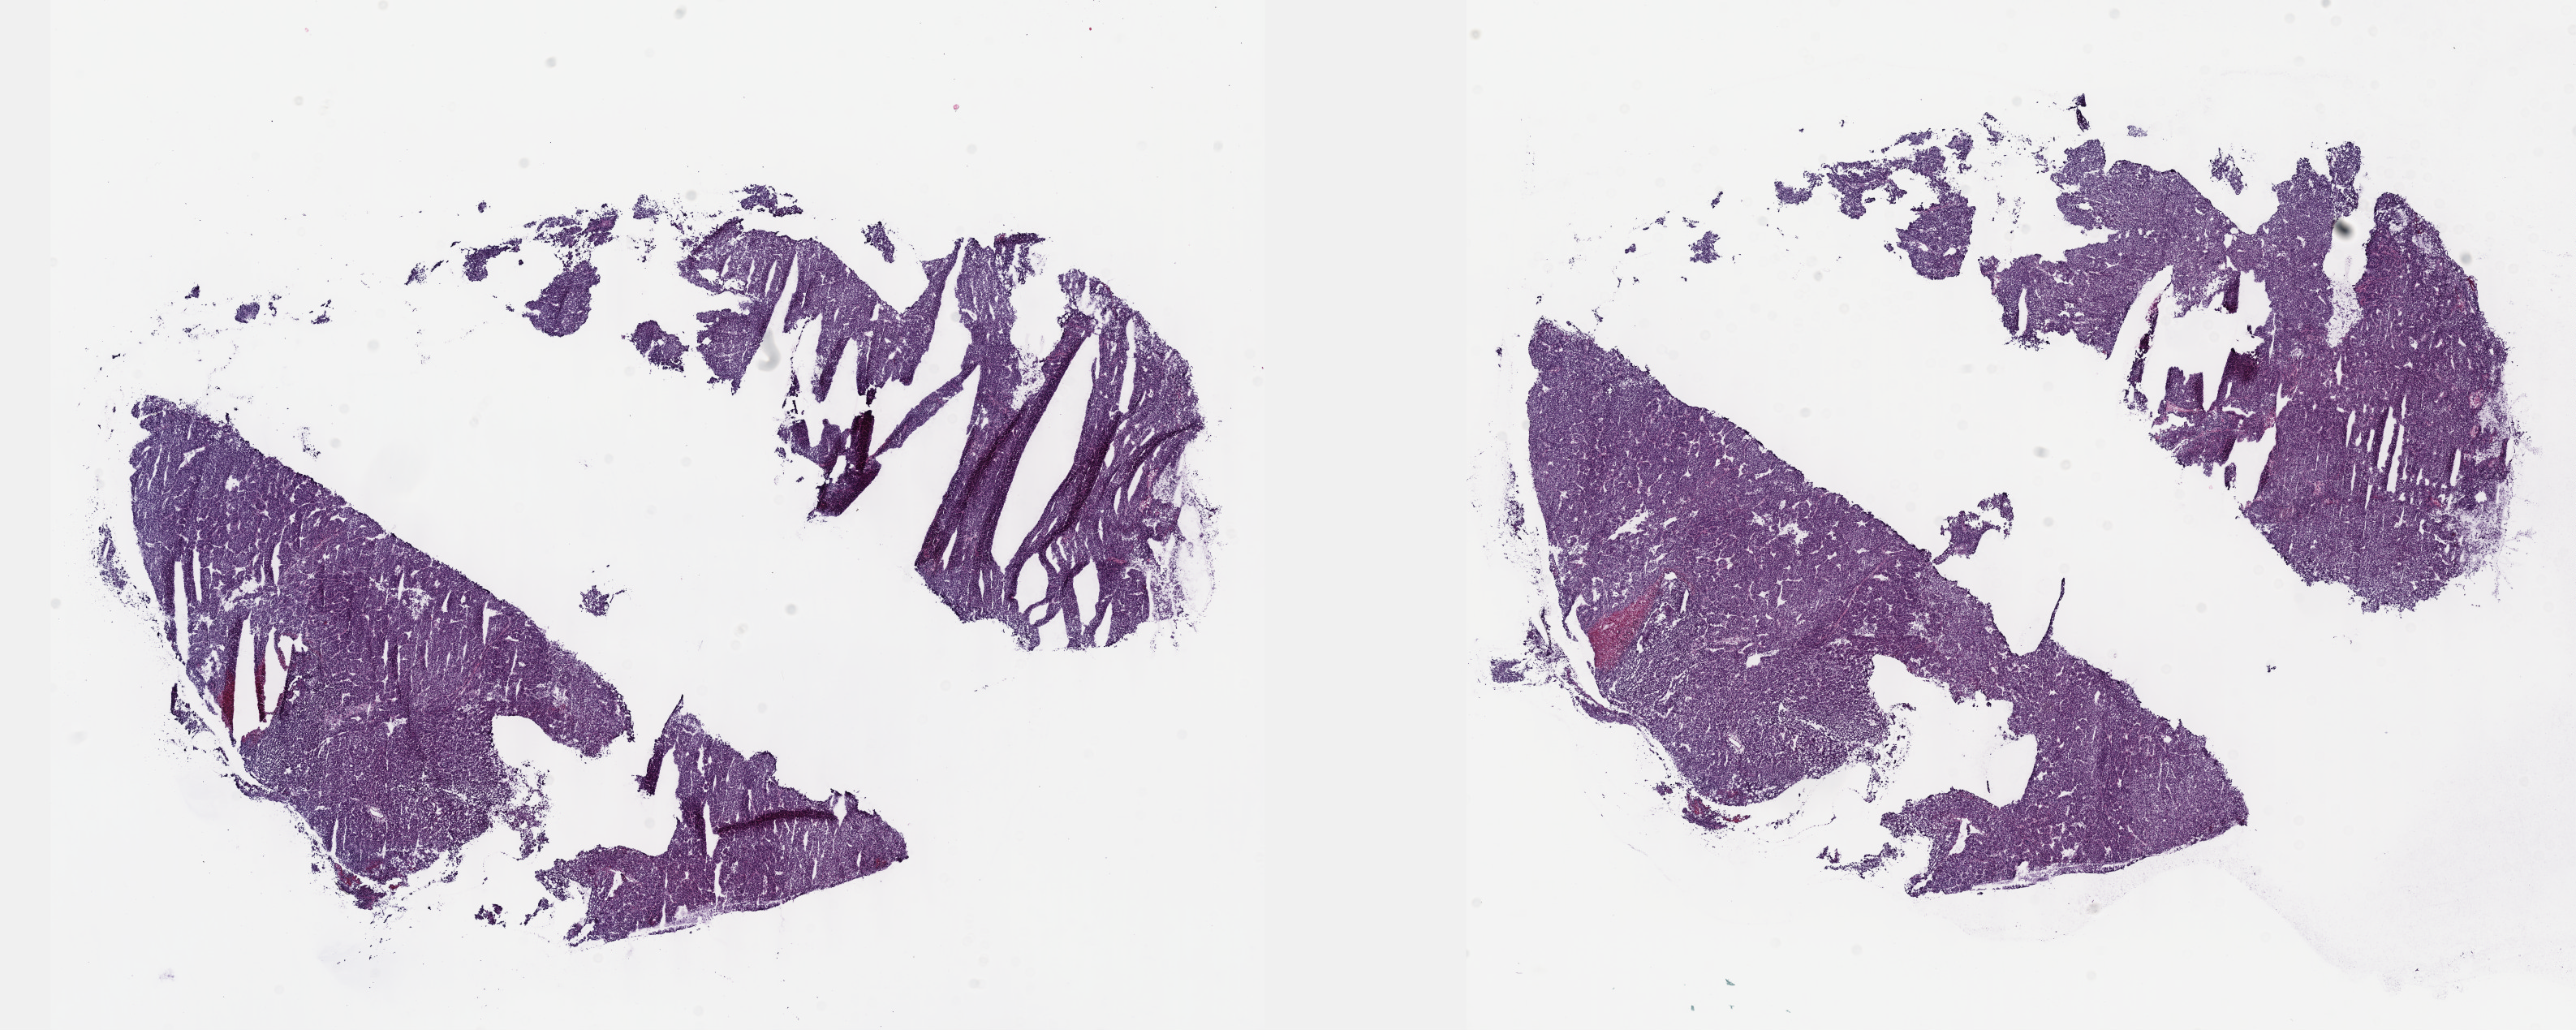
Whole-slide histology image, H&E-stained — shown as a low-resolution overview of the whole scanned area (about 25.7 x 10.3 mm, from a 40x scan), frozen section, liver, primary tumour sample. Female, age 66 years at initial diagnosis. Histologic grade: G3 (poorly differentiated). Pathologist review of this section (percent, as recorded): tumour cells 80%, tumour nuclei 80%, normal cells 0%, stromal cells 17%, necrosis 3%. Infiltration values recorded for this section: lymphocyte infiltration 3%, monocyte infiltration 1%, neutrophil infiltration 2%.
TNM: T4 N0 M0. Diagnosis: Hepatocellular carcinoma, NOS. AJCC pathologic stage: IIIC (7th edition).